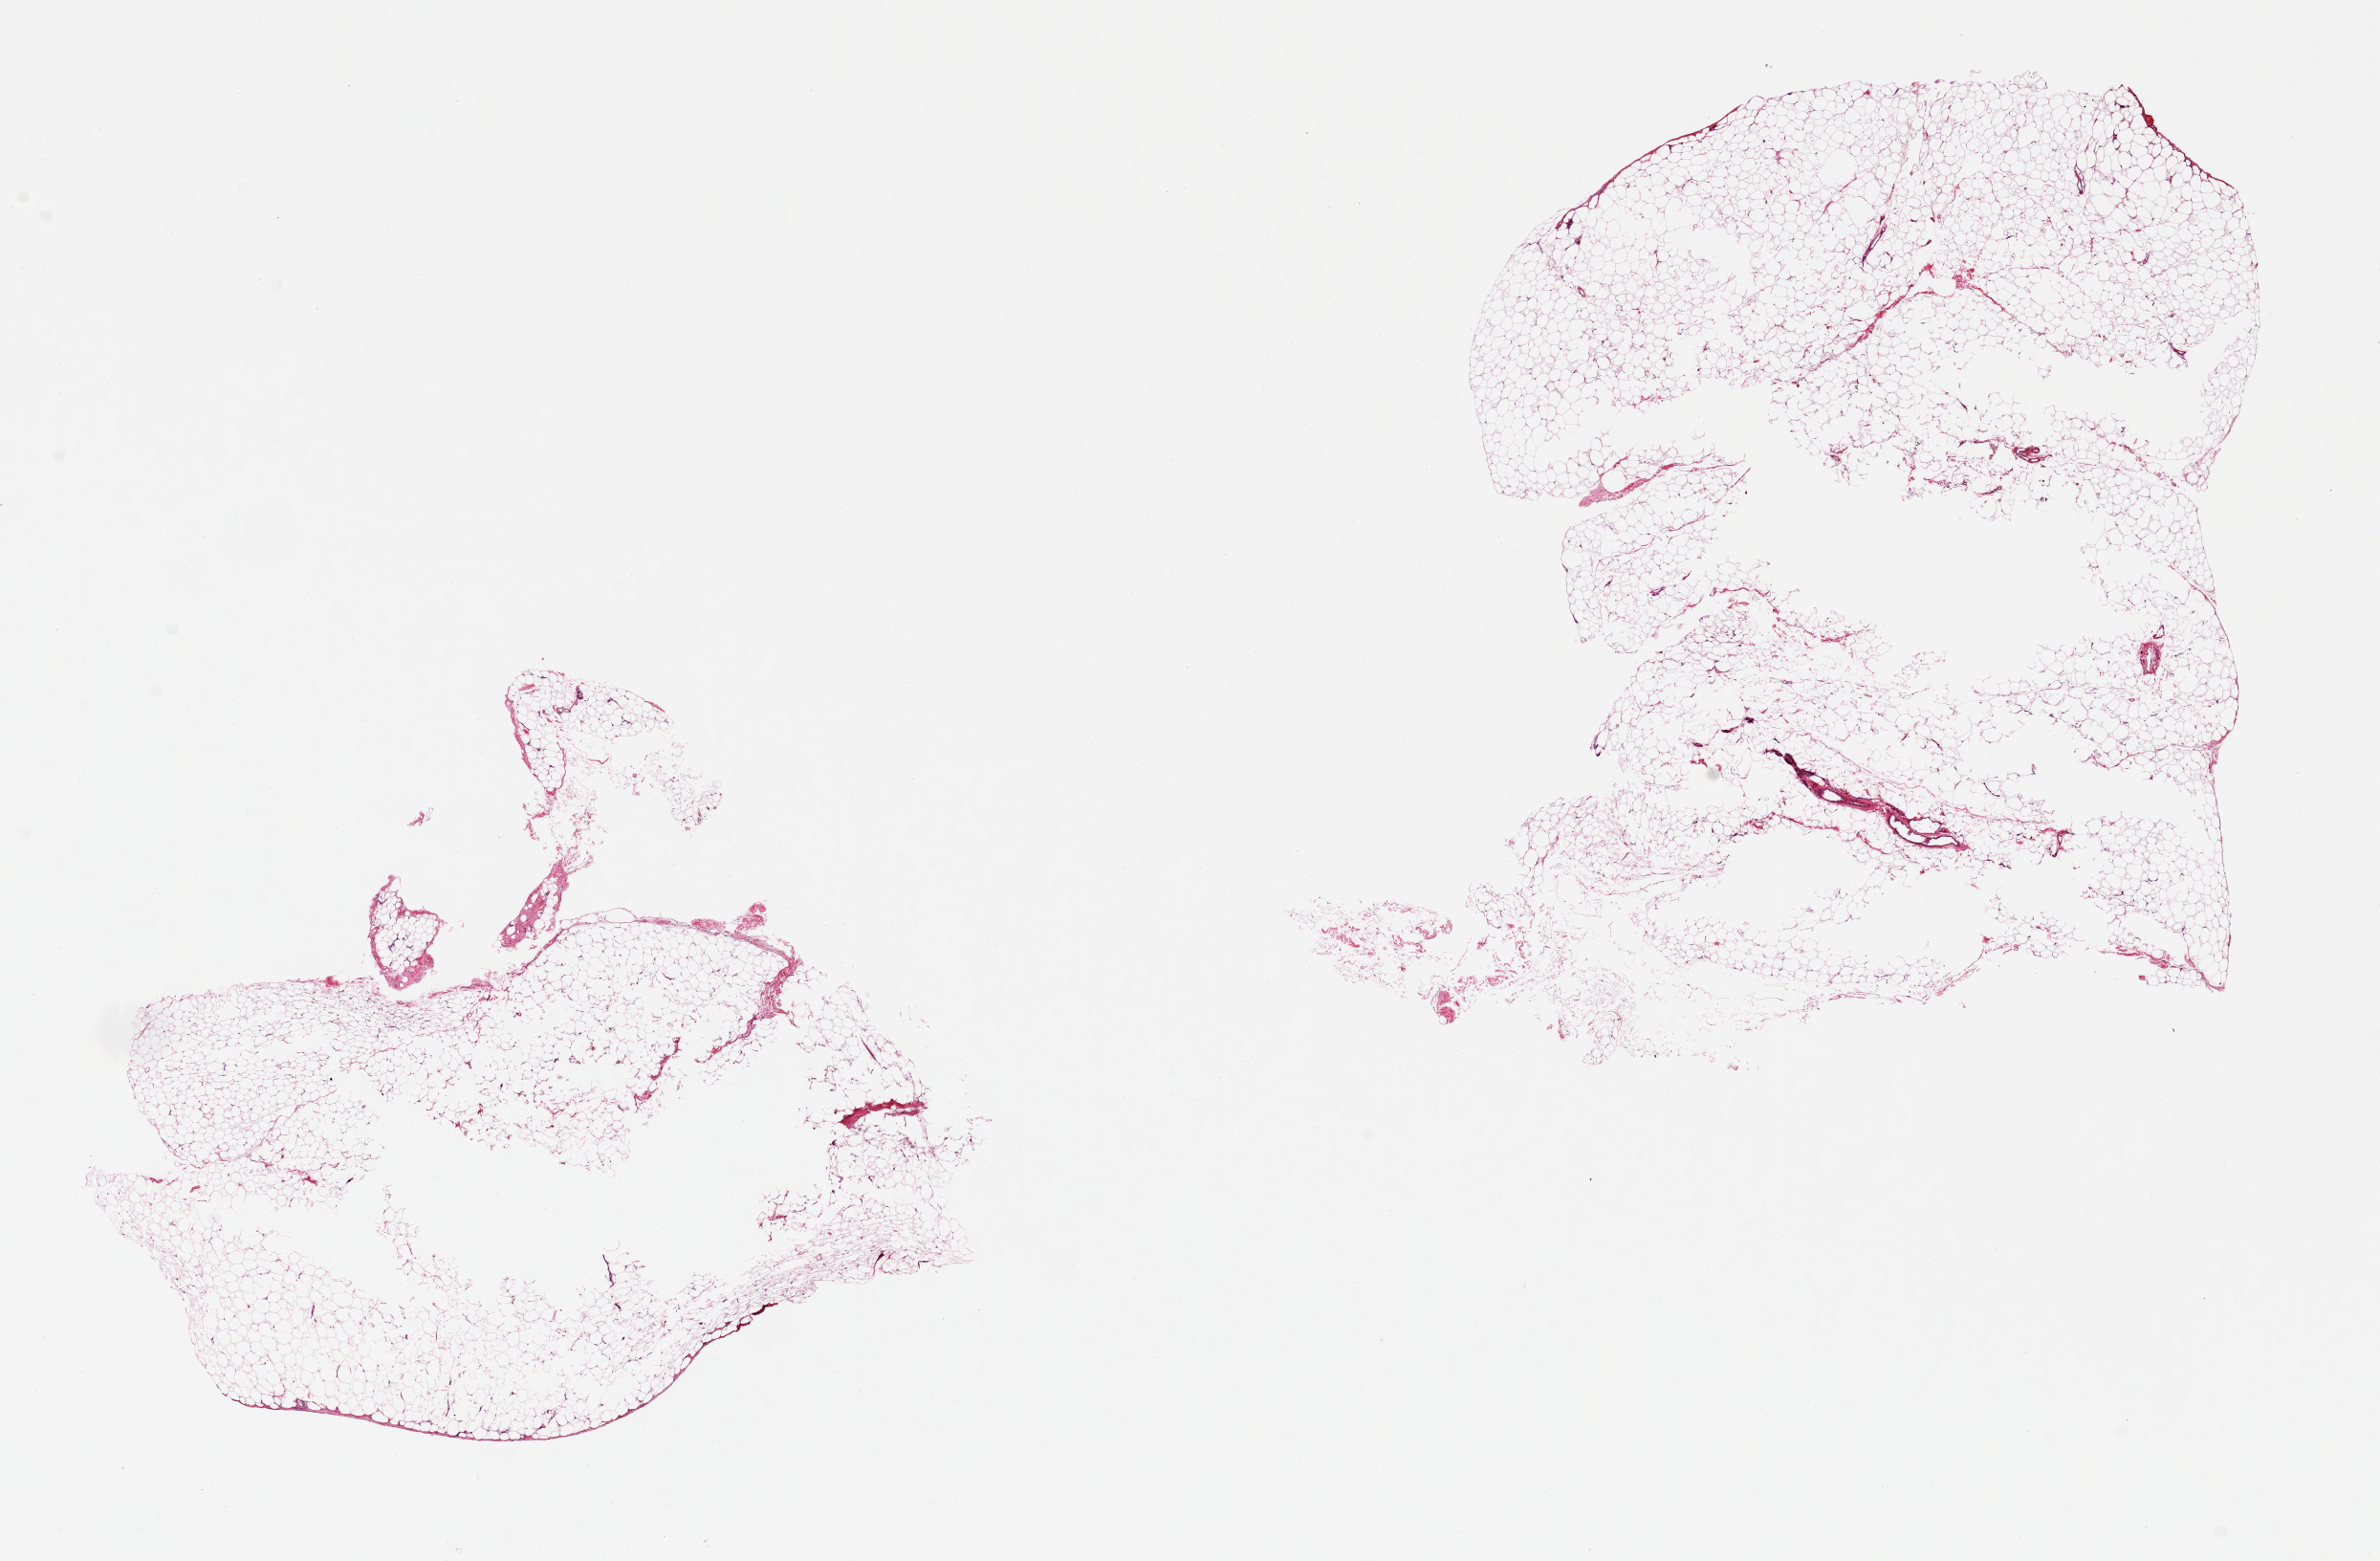
Digitized H&E-stained section, brightfield — shown as a low-resolution overview of the whole scanned area (about 19.7 x 12.9 mm, acquisition: 20x scan), PAXgene-fixed paraffin-embedded (PFPE) section, target tissue: omentum, donor tissue sample. Male donor.
Reviewer comment on this tissue sample: 2 pieces, 7x6 & 8x7.5mm; central unfixed holes up to 3mm across.